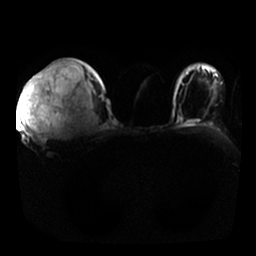
Breast MRI, one axial slice; position 17 of 25 along the scan axis; diffusion-weighted series; image 2 of 4 stored at this slice position (different b-values; order by instance number); 1.5 T; 4 mm slice thickness; 256 × 256 image matrix, field of view 350 × 350 mm. Female patient.
Structures marked on this image (manually delineated by an expert):
- tumour on diffusion-weighted imaging: bounding box [x1, y1, x2, y2] px = [21, 77, 62, 140]